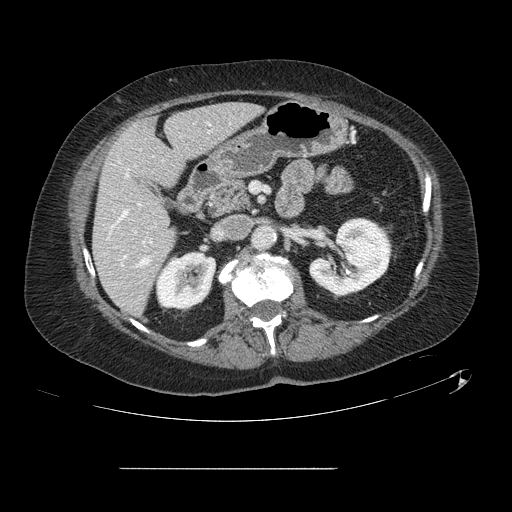
Contrast-enhanced abdominal CT, one axial slice. Position 55 of 148 along the scan axis. Intravenous contrast given. Soft-tissue window (W 400 / L 40 HU). 512 × 512 image matrix. Female patient, age 75 years. Case-level facts recorded for this patient, not image findings: diagnosis: colorectal cancer liver metastases, imaged before liver resection; multiple liver metastases: no; largest metastasis: 2.4 cm.
Outlined on this slice (outlined manually by an expert reader):
- hepatic veins: box from (x=112, y=174) to (x=149, y=266) px
- liver: (x=94, y=105)–(x=260, y=315)
- planned liver remnant (the part of the liver to remain after resection): (x=94, y=105)–(x=259, y=315)
- portal vein (with intrahepatic branches): (x=124, y=204)–(x=140, y=258)